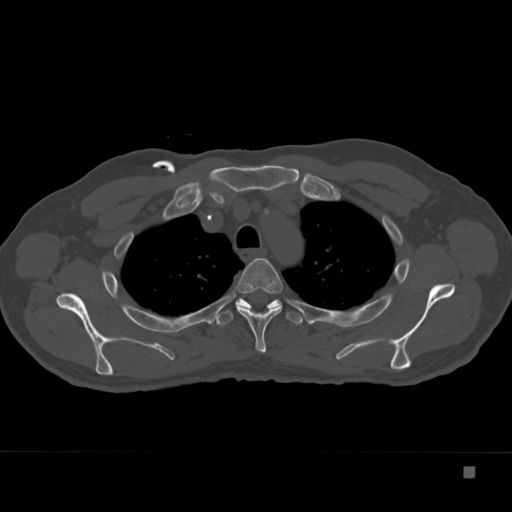
CT including the spine, one axial slice. Position 281 of 332 along the scan axis. Reconstruction kernel Br40s. 120 kVp. Bone window (W 1800 / L 400 HU). 512 × 512 image matrix, field of view 389 × 389 mm. Patient: male, 72 years. Case-level facts recorded for this patient, not image findings: primary cancer: skeletal.
Structures marked on this image (semi-automatic segmentation, software-assisted and operator-edited):
- T3 vertebra: bounding box [x1, y1, x2, y2] px = [235, 258, 283, 353]
- T4 vertebra: [214, 297, 305, 326]